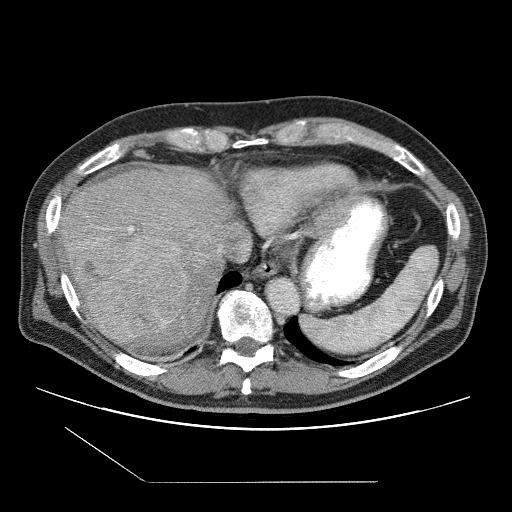
Contrast-enhanced abdominal CT (liver protocol), one axial slice; position 85 of 109 along the scan axis; one of 2 acquisitions stored at this slice position; soft-tissue window (W 400 / L 40 HU); 2.5 mm slice thickness; 512 × 512 image matrix. Case-level facts recorded for this patient, not image findings: diagnosis: hepatocellular carcinoma (patient treated with transarterial chemoembolisation; whether this scan precedes or follows treatment is not stated here); TNM stage (as recorded): Stage-IIIB; Child-Pugh class: A; tumour differentiation: well differentiated.
Annotated regions visible in this slice (semi-automatically segmented with operator editing):
- liver parenchyma outside the tumour (the mass and vessels are separate outlines, so this box may not span the whole liver): bounding box [x1, y1, x2, y2] px = [56, 166, 294, 344]
- mass: [68, 232, 193, 344]
- liver vessels: [103, 226, 219, 252]